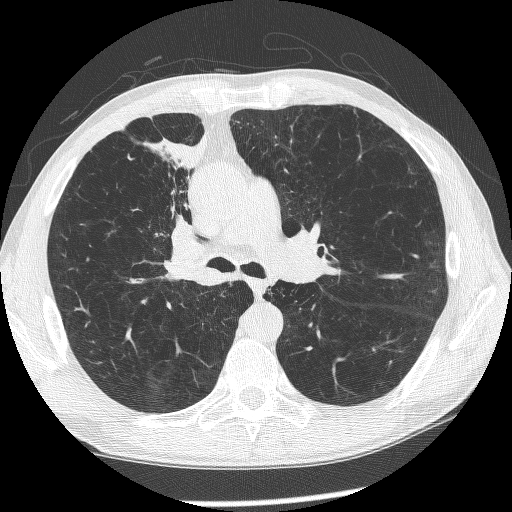
Axial slice from a low-dose chest CT screening exam. Baseline annual screen. Lung window (W 1500 / L -600 HU). 120 kVp. Male participant, aged 60 years at enrolment. Current smoker at enrolment.
Expert-annotated lung lesion, bounding box (x1, y1, x2, y2) in pixels: (145, 197, 222, 290). Screening reader's record for this exam (one nodule recorded; not confirmed to be the boxed lesion): non-calcified nodule or mass ≥4 mm, right upper lobe, 12 × 8 mm, spiculated (stellate) margins, mixed attenuation. Official screen result: positive, change unspecified: nodule(s) >= 4 mm or enlarging nodule(s), mass(es), or other non-specific abnormalities suspicious for lung cancer. Later outcome: lung cancer diagnosed 208 days after this screen — squamous cell carcinoma, NOS, right upper lobe, right middle lobe, right main stem bronchus, poorly differentiated (G3), stage IV (AJCC 6th edition).